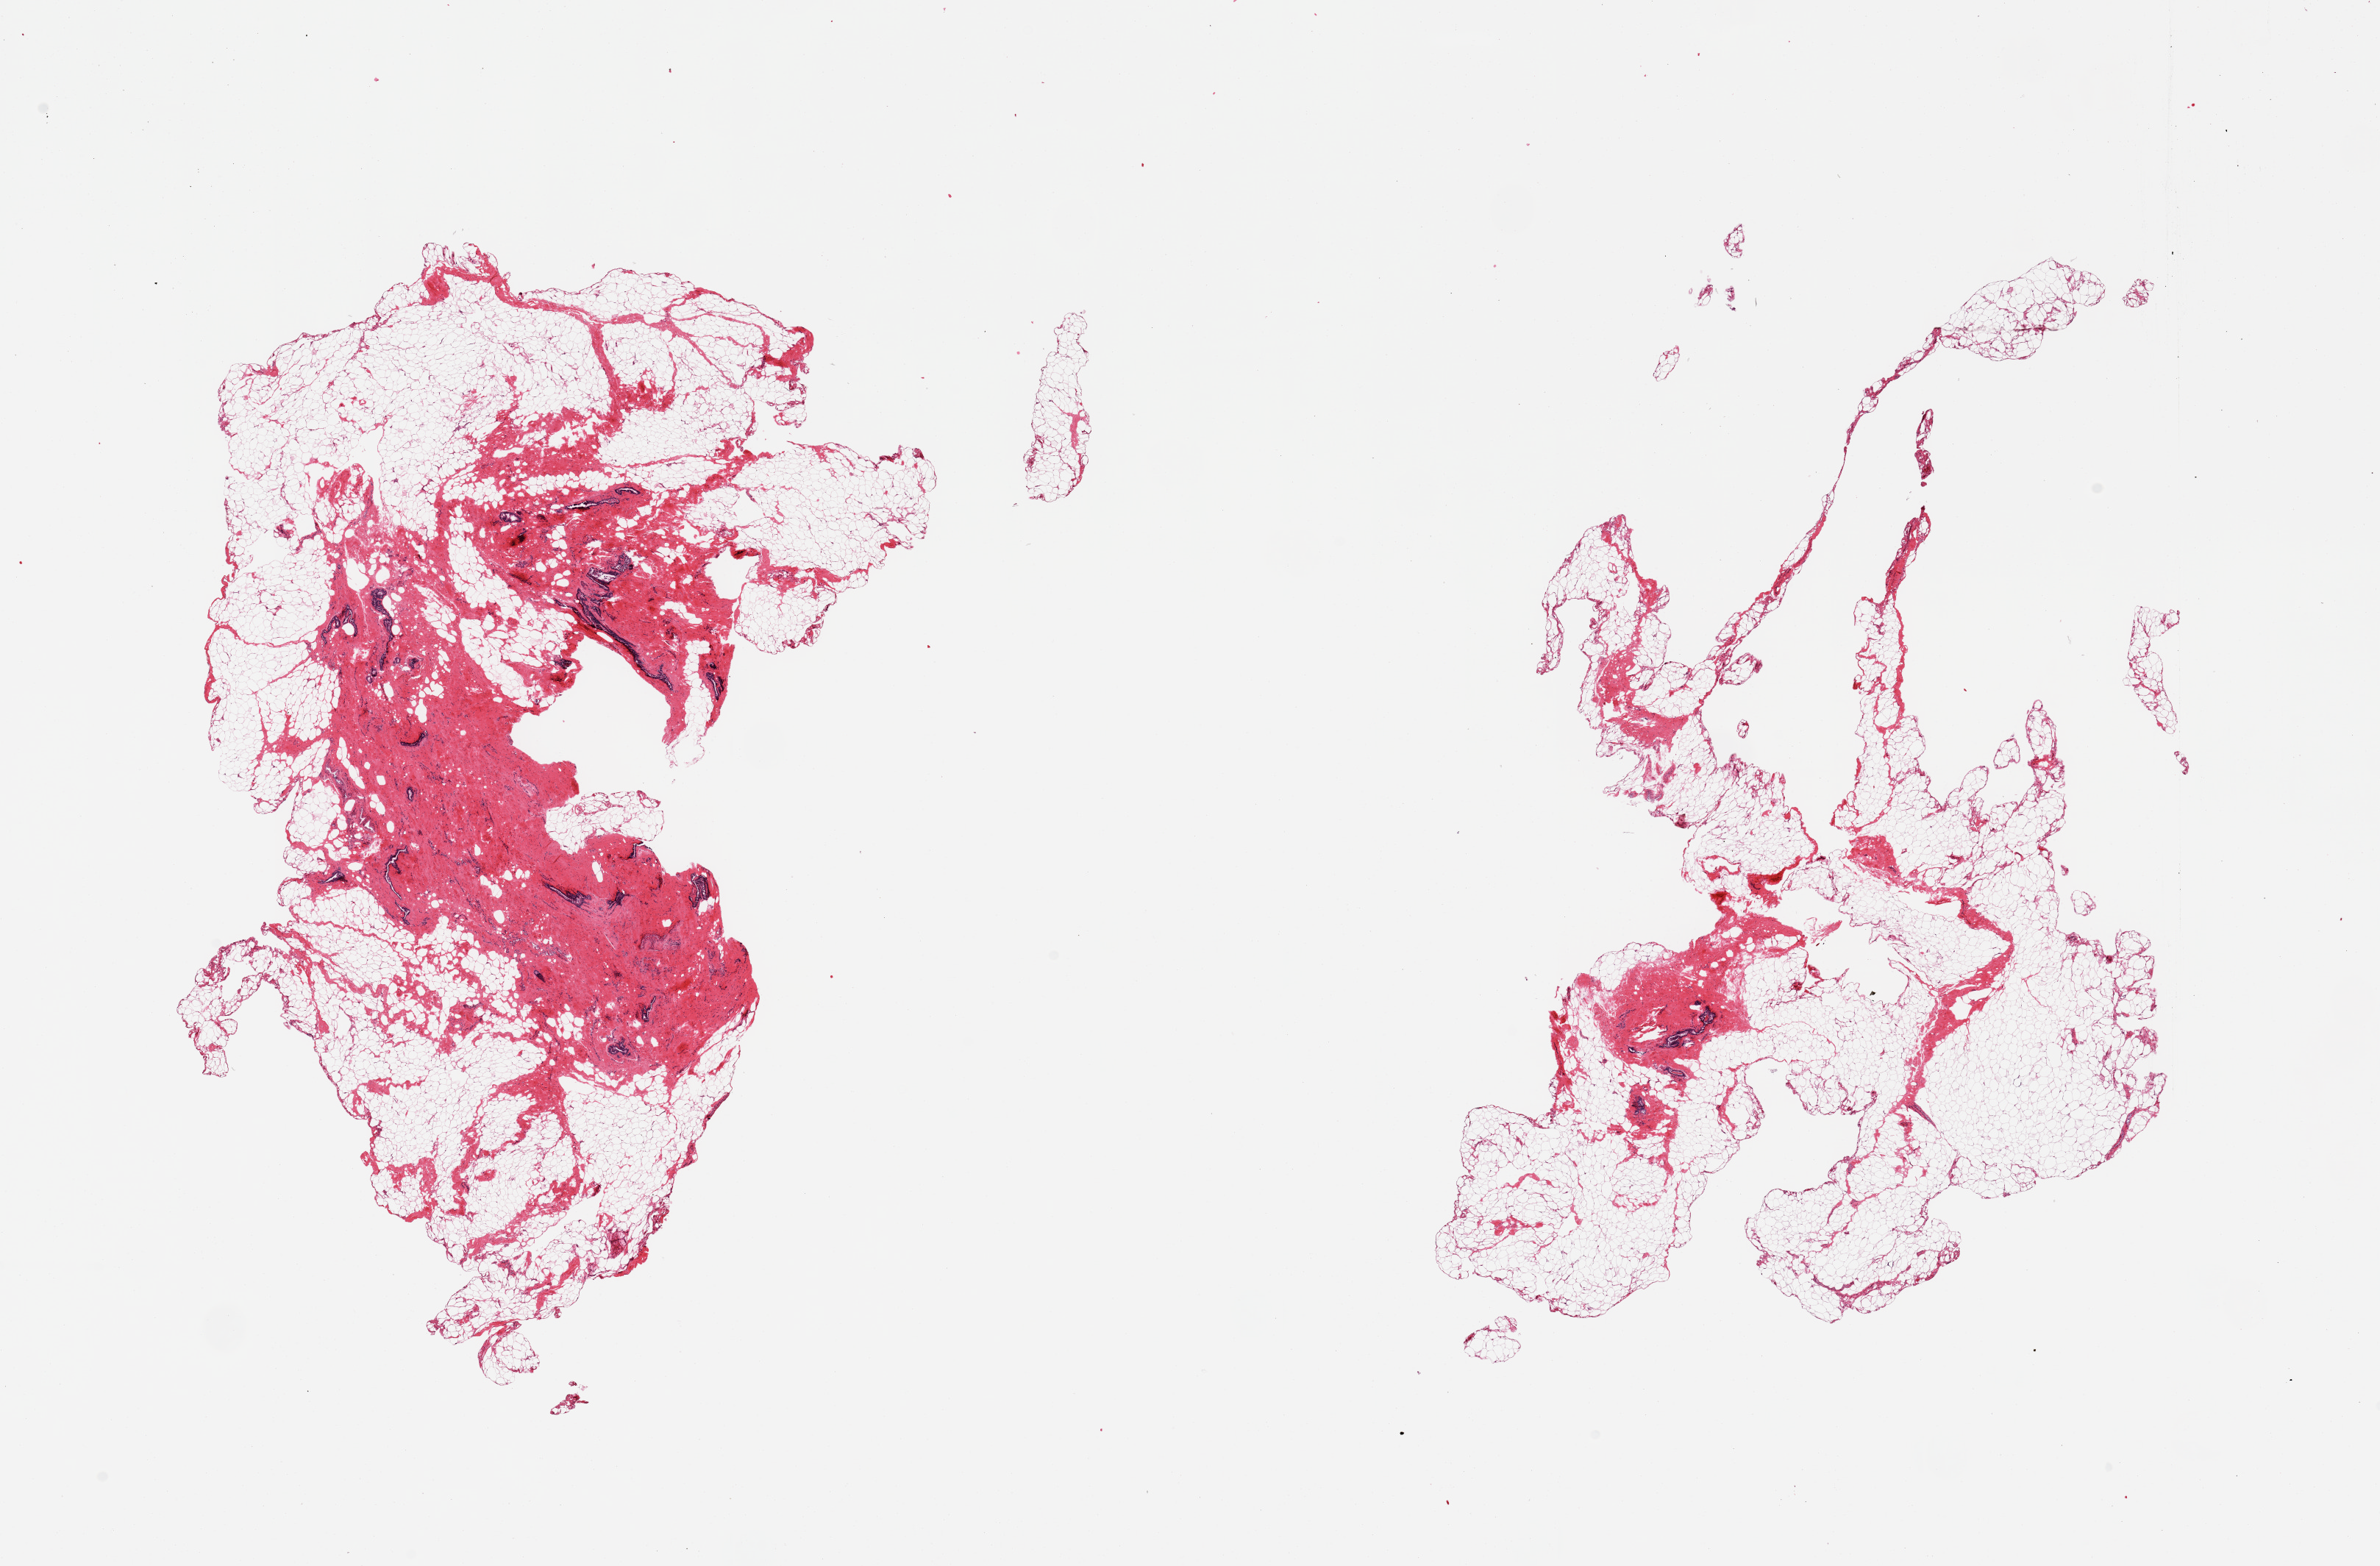
Whole-slide image, haematoxylin and eosin stain, low-resolution overview of the scanned area, about 25.6 x 16.8 mm (slide scanned at 20x), PAXgene-fixed, paraffin-embedded tissue, target tissue: breast, tissue donor sample. Donor sex: male.
• review note (as recorded): 2 pieces; ducts in fibrous stroma with 60 & 80% fat